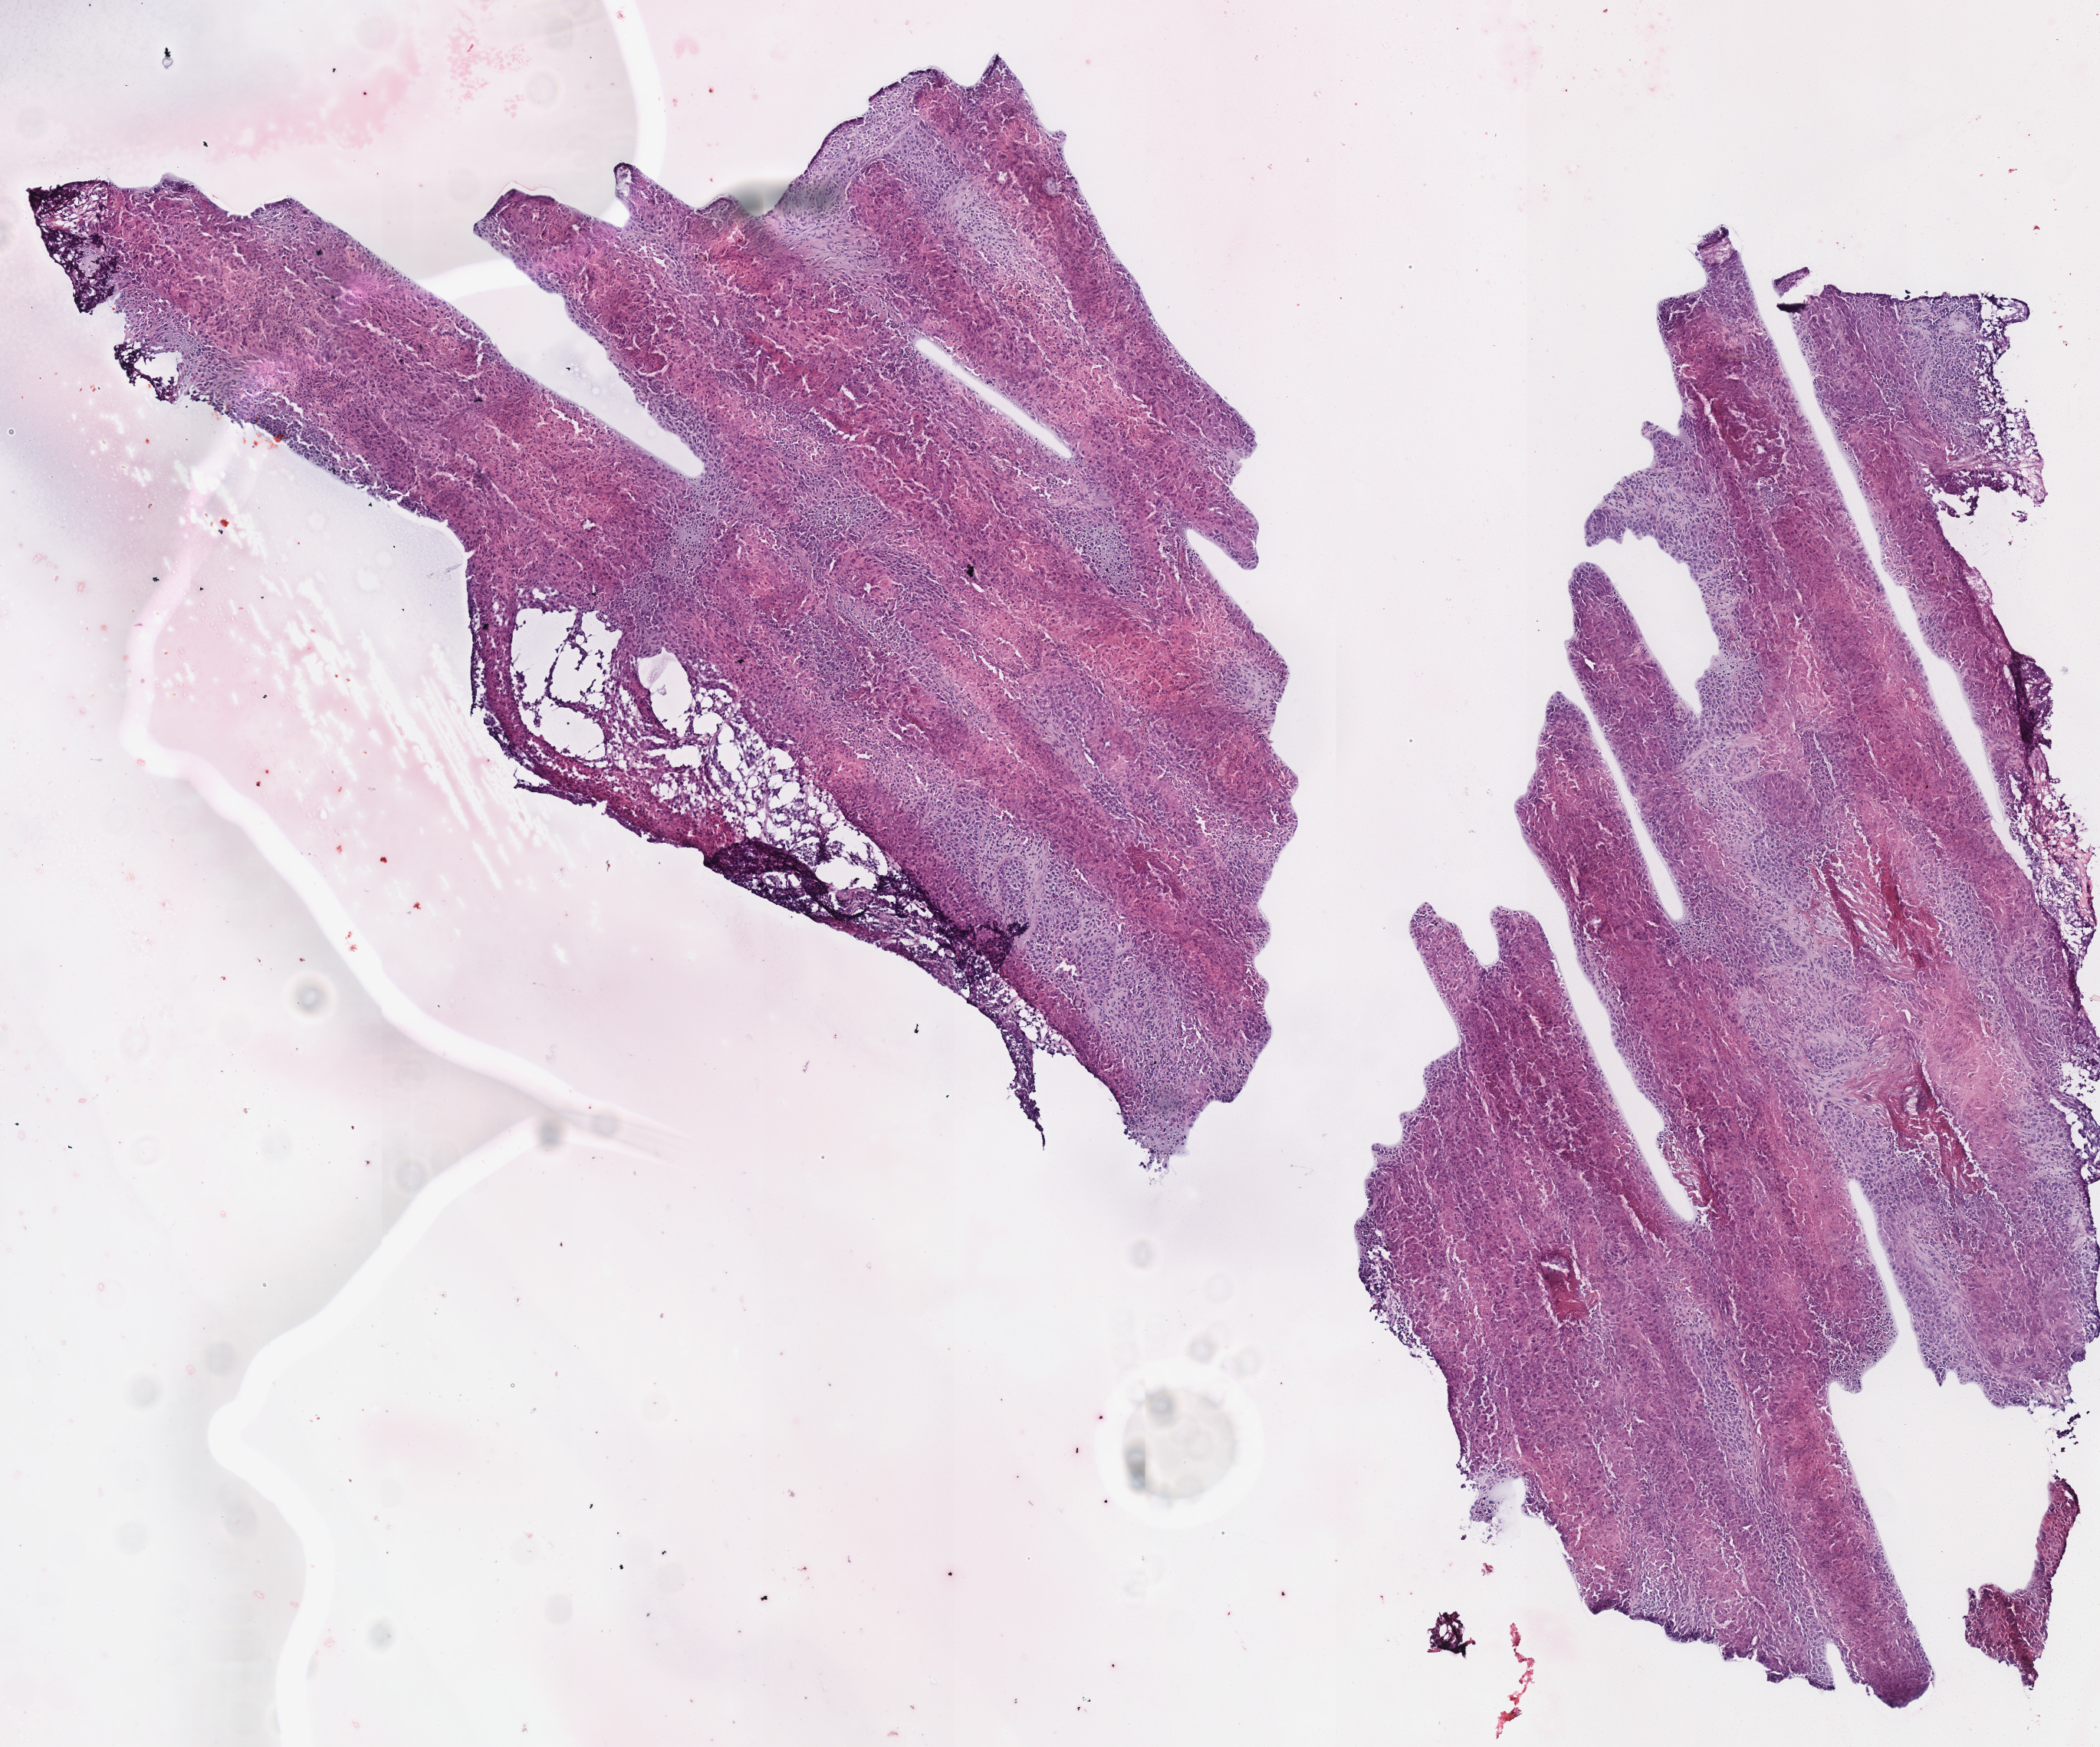
Hematoxylin and eosin (H&E) stained whole-slide image, whole scanned area (about 5.4 x 4.5 mm) shown as a low-resolution overview, frozen section, sample: primary tumour, lung. Male, age 60 years at initial diagnosis.
Pathologic diagnosis: Squamous cell carcinoma, NOS (lower lobe, lung).